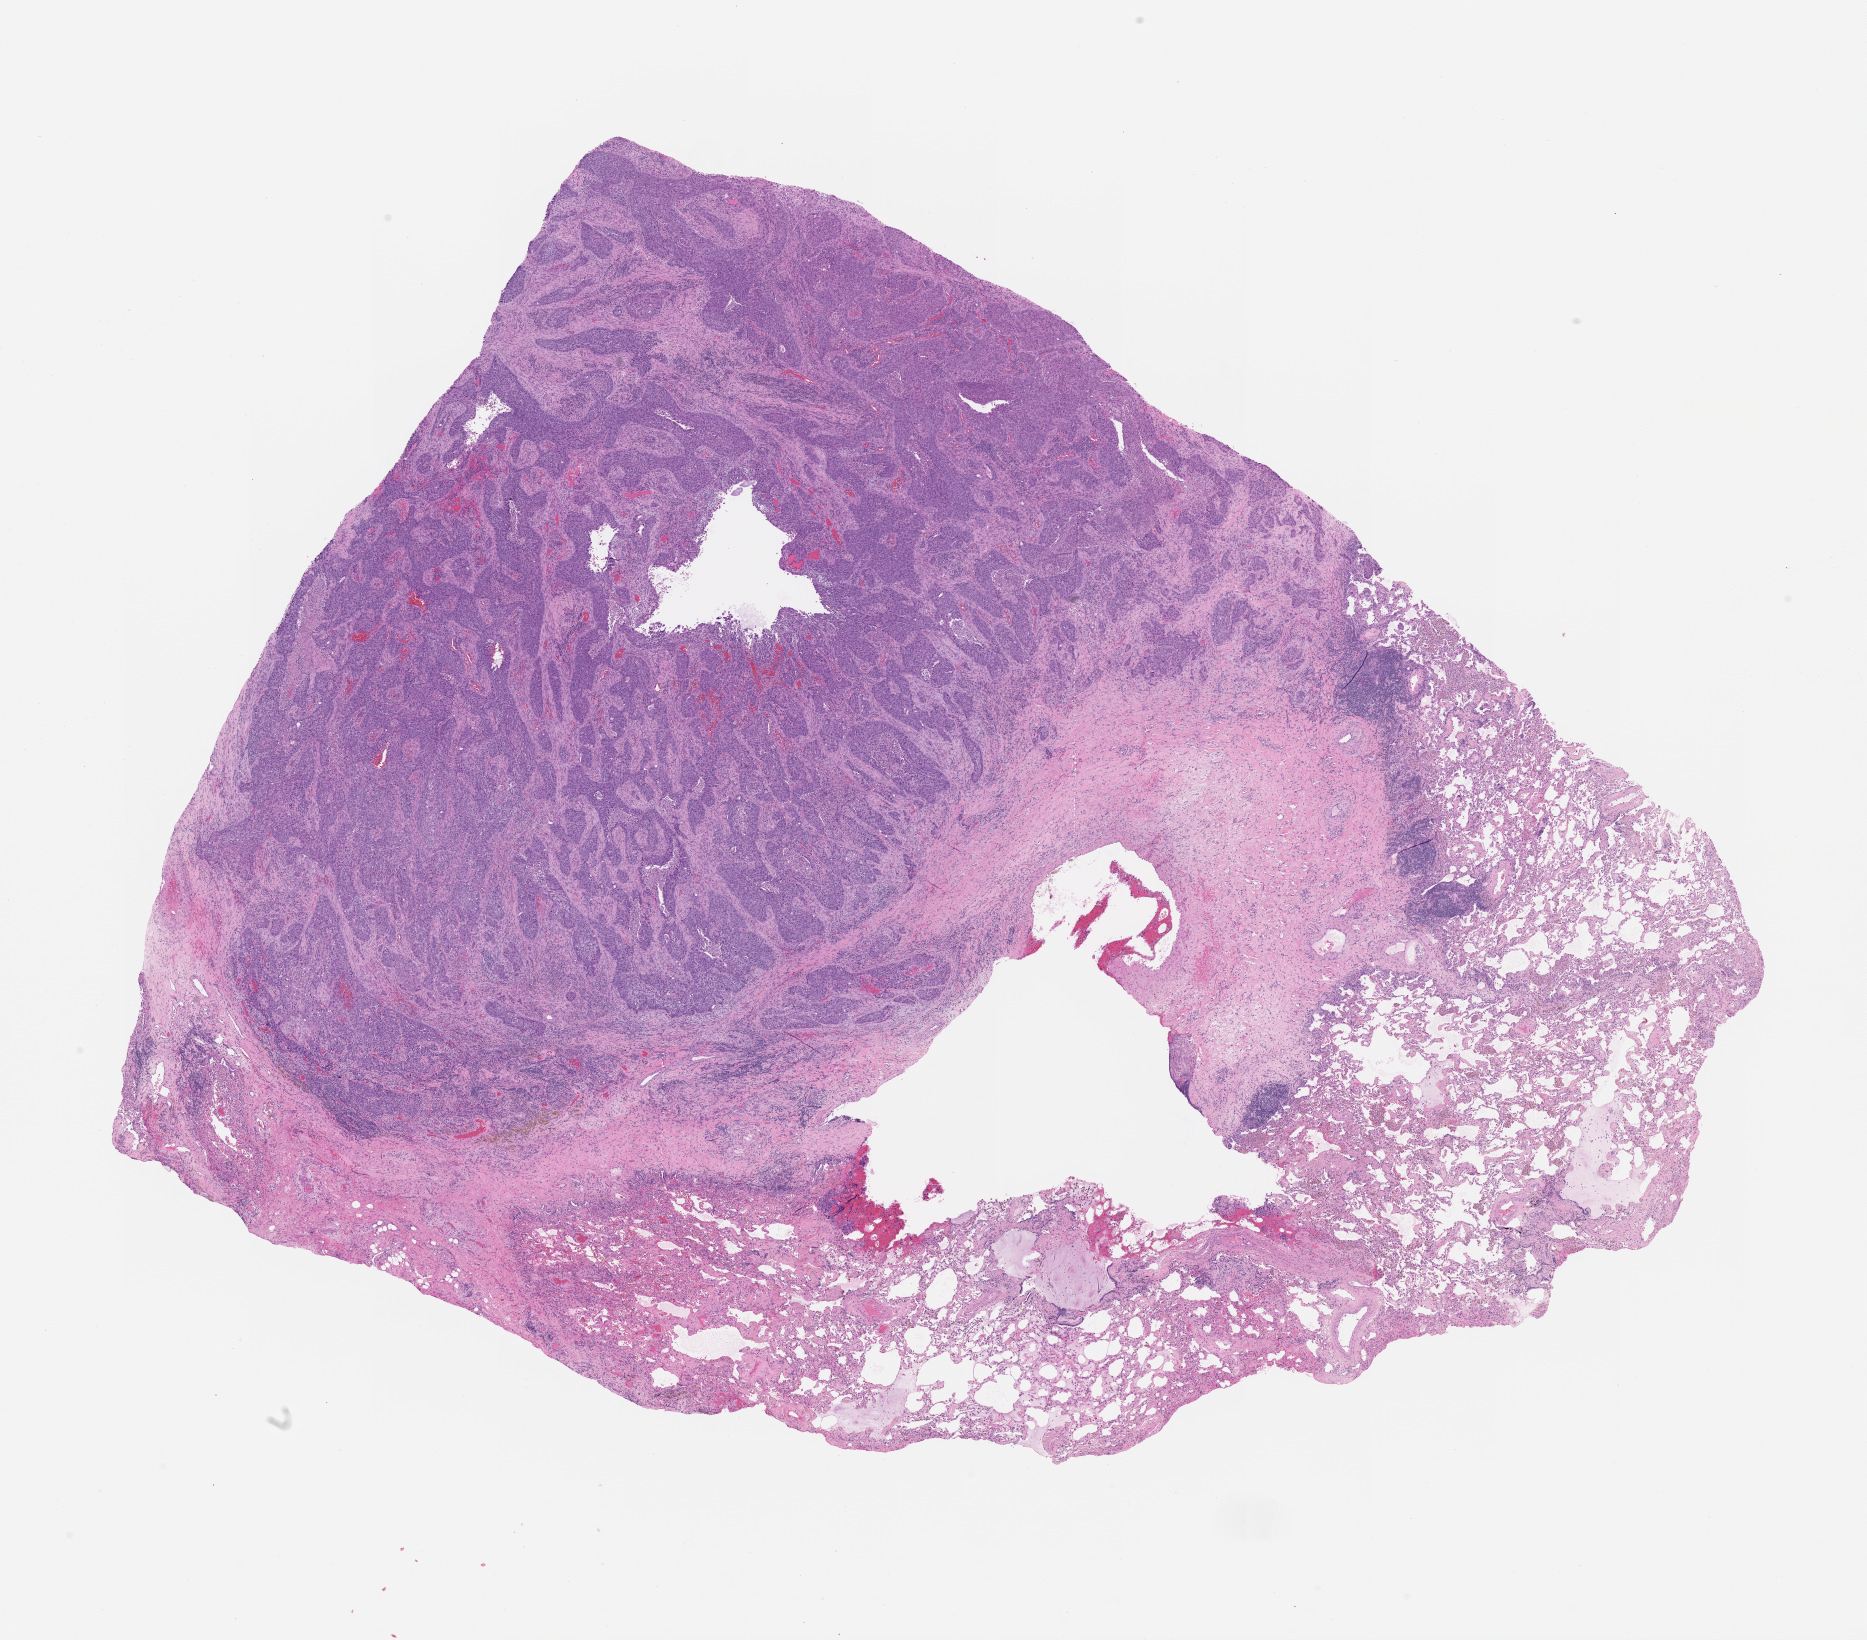
Digitized Hematoxylin and eosin (H&E) stained tissue section (whole slide) — shown as a low-resolution overview of the whole scanned area (about 15.0 x 13.2 mm, slide scanned at 20x); tumour tissue sample, lung. Female, 54 y/o.
• patient diagnosis (cohort enrolment): squamous cell carcinoma (lung)